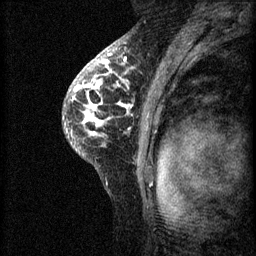
Breast MRI (dynamic contrast-enhanced), one sagittal slice. Position 45 of 60 along the scan axis. 3 images stored at this slice position (order not interpretable as contrast timing). 1.5 T. TE 4.2 ms, TR 8.2 ms. 256 × 256 image matrix, field of view 180 × 180 mm. Female patient, age 41 years.
Outlined on this slice (semi-automatic segmentation, software-assisted and operator-edited):
- analysis volume of interest (the breast-tissue region the enhancement analysis was run in; not a lesion): bounding box <62,62,157,175> (left, top, right, bottom; pixels)
- tumour enhancement mask (voxels above the 70 % enhancement threshold inside the analysis volume of interest): <69,62,132,137>